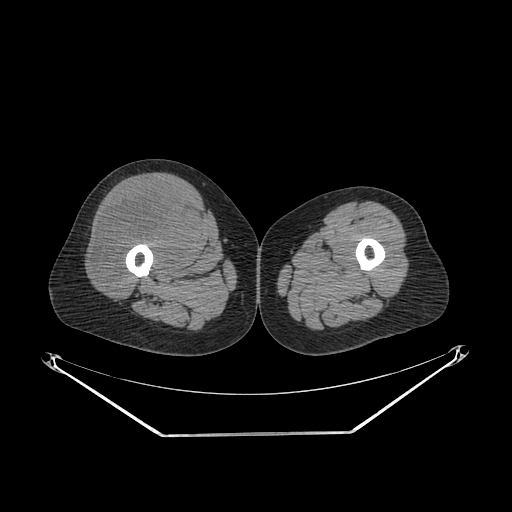
CT of an extremity soft-tissue mass (from a PET/CT study), one axial slice. Position 245 of 311 along the scan axis. 140 kVp. Soft-tissue window (W 400 / L 40 HU). 512 × 512 image matrix, field of view 500 × 500 mm. Female patient. From the clinical record (not read from this slice): histological type: pleiomorphic undifferentiated sarcoma; grade: high; site of the primary tumour: right quadricep.
Outlined on this slice (expert contour drawn on MRI and transferred to this co-registered scan by the dataset authors):
- tumour plus oedema (research contour): bounding box <96,187,195,284> (left, top, right, bottom; pixels)
- tumour (research contour): <96,187,195,284>